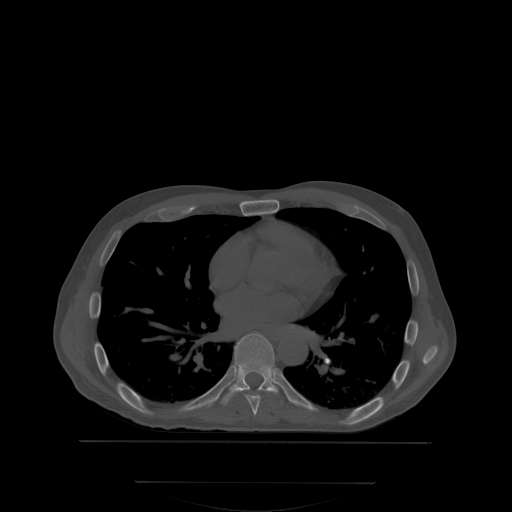
CT including the spine, one axial slice; slice 220 of 350 in the series (ordered by position); bone window (W 1800 / L 400 HU); 512 × 512 image matrix, field of view 500 × 500 mm. Patient: male, 58 years. From the clinical record (not read from this slice): primary cancer: prostate; vertebrae with lytic lesions (as recorded): L1.
Outlined on this slice (semi-automatic segmentation, software-assisted and operator-edited):
- T7 vertebra: bounding box <246,394,260,415> (left, top, right, bottom; pixels)
- T8 vertebra: <221,333,279,404>